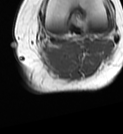
MRI of an extremity soft-tissue mass, one axial slice. Slice 50 of 68 in the series (ordered by position). MR volume resampled by the dataset authors to the PET/CT grid (not the native acquisition matrix). 3.27 mm slice thickness. 123 × 134 image matrix, field of view 120 × 131 mm. Female patient. From the clinical record (not read from this slice): histological type: extraskeletal high grade osteogenic sarcoma; grade: high; site of the primary tumour: left calf.
Structures marked on this image (expert contour drawn on MRI and transferred to this co-registered scan by the dataset authors):
- gross tumour volume (mass): bounding box <45,46,71,69> (left, top, right, bottom; pixels)